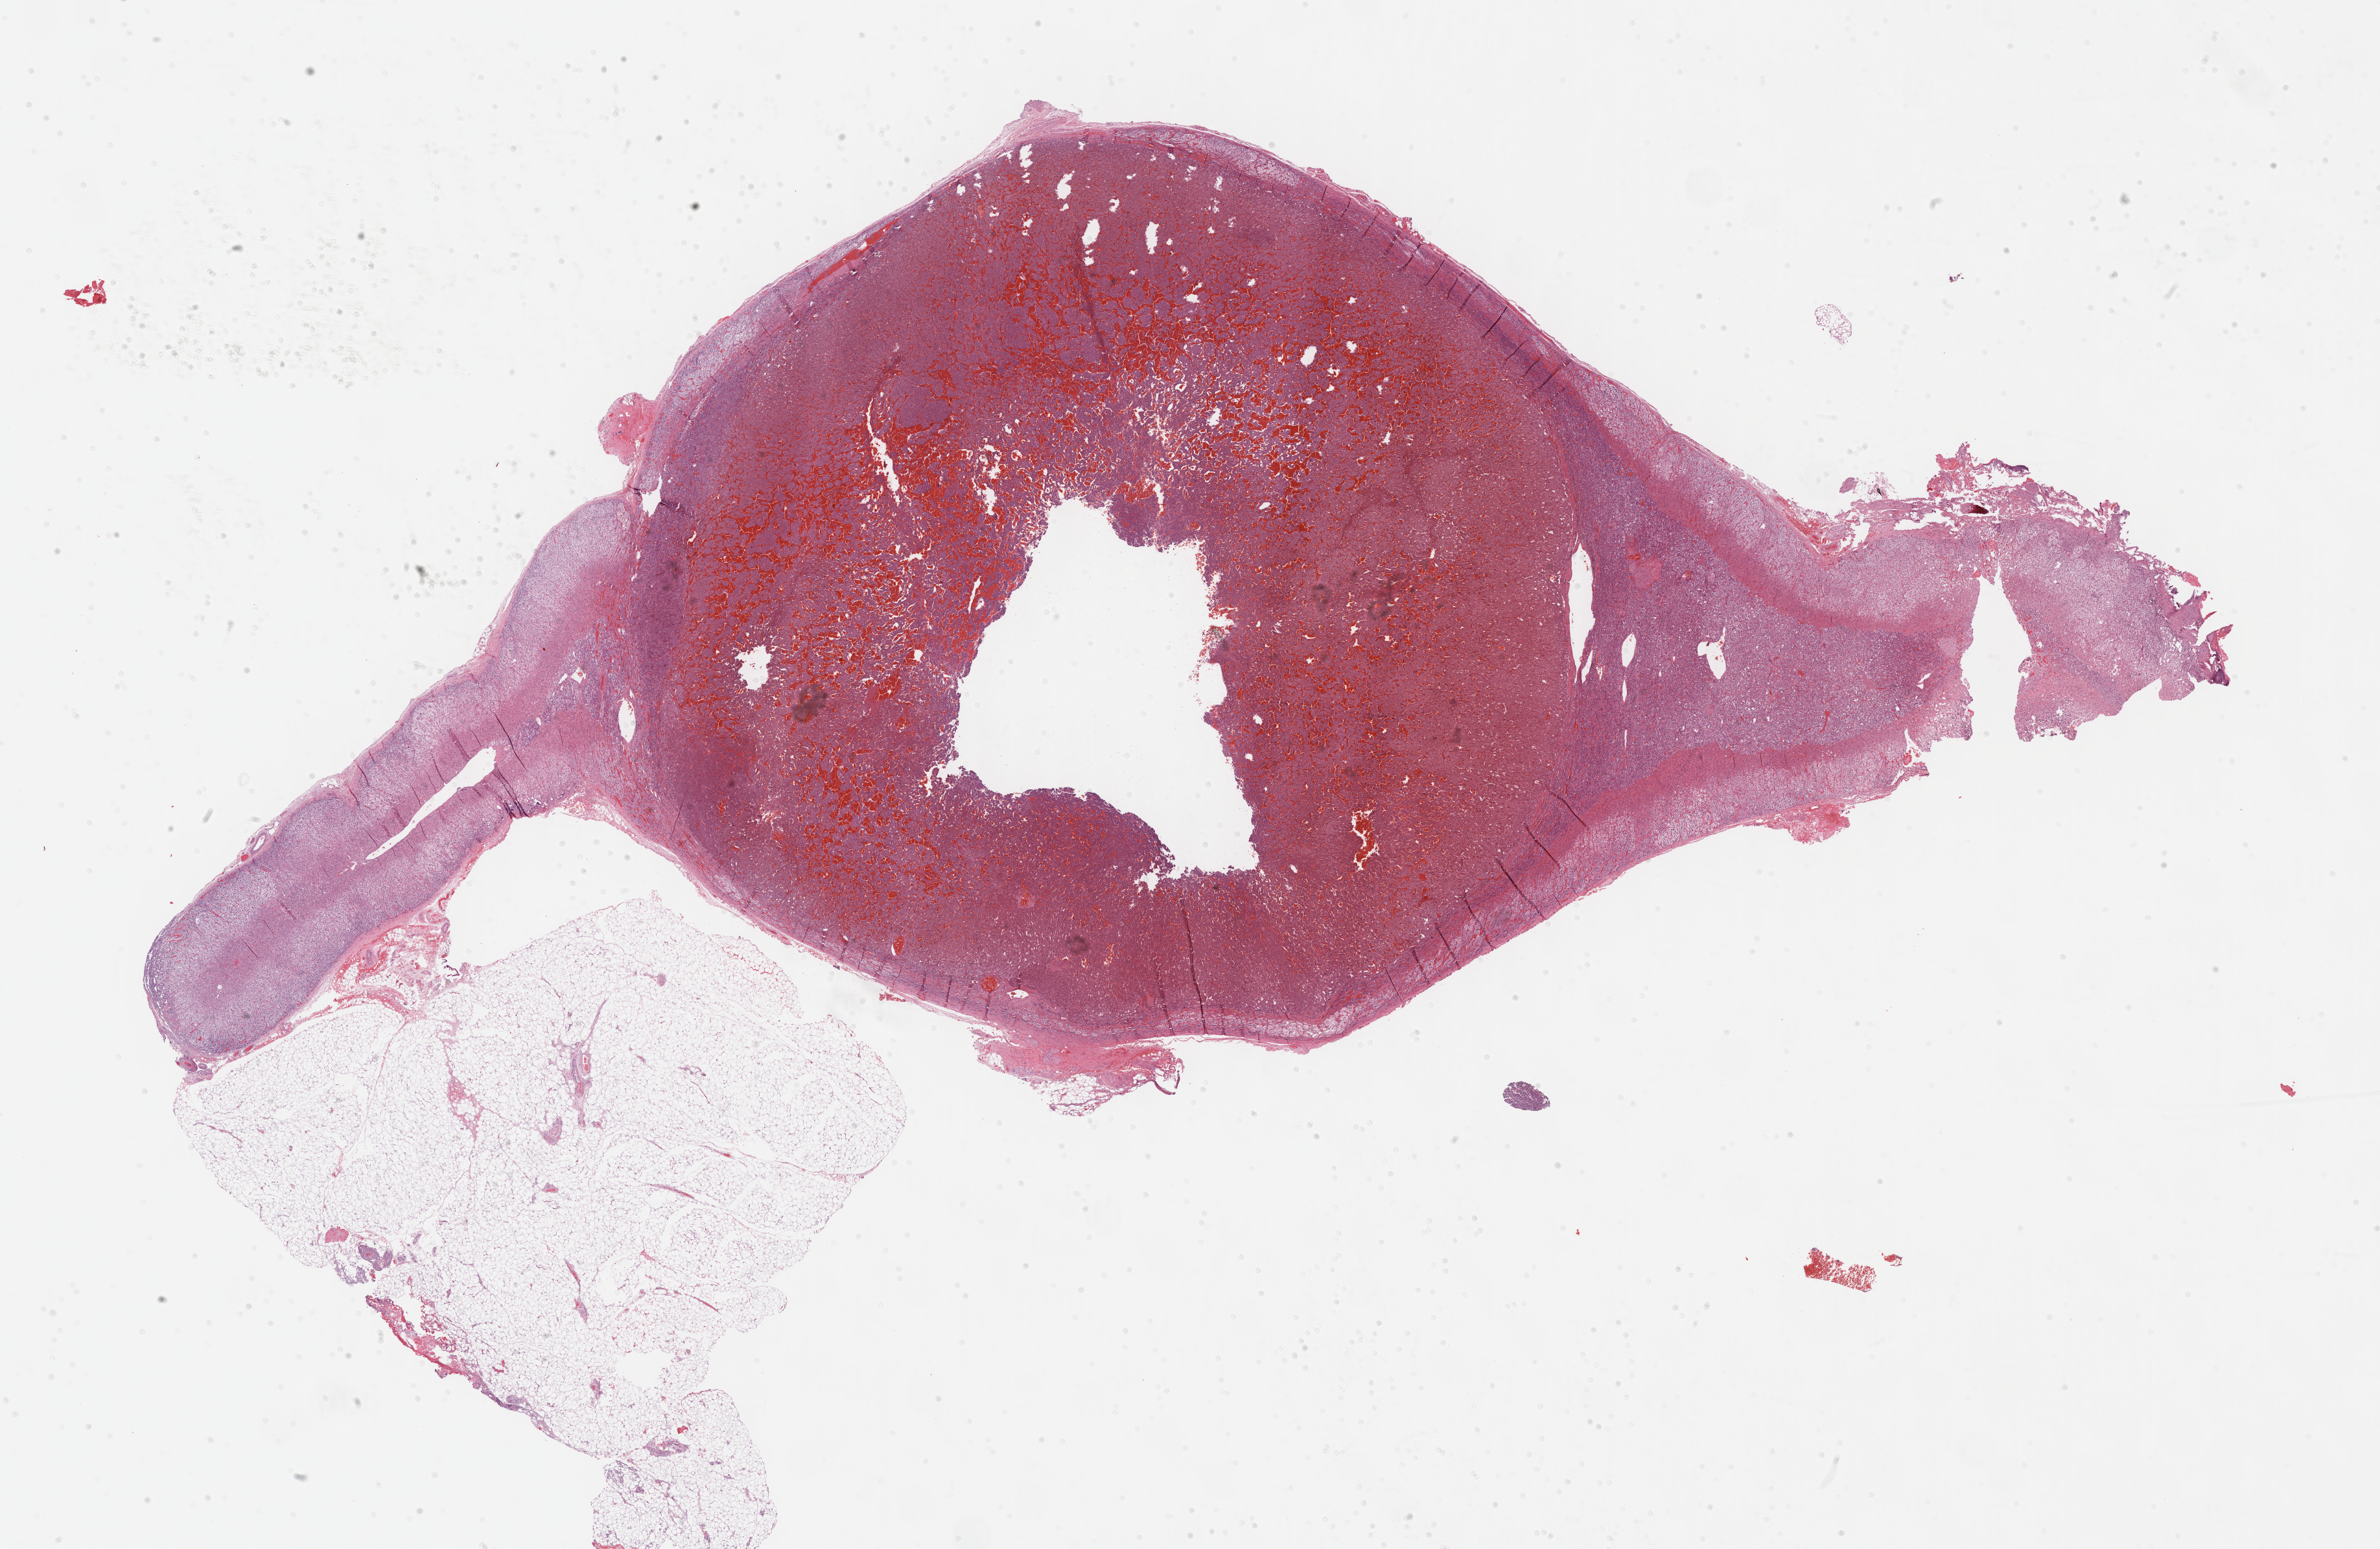
Digitized H&E-stained tissue section (whole slide), a low-resolution overview of the entire scanned area, about 29.7 x 19.3 mm (acquisition: 40x scan). Formalin-fixed paraffin-embedded (FFPE) diagnostic section. Sample: primary tumour, adrenal gland. Male, age 31 years at initial diagnosis.
Histologic diagnosis: Medullary carcinoma, NOS (thyroid gland).